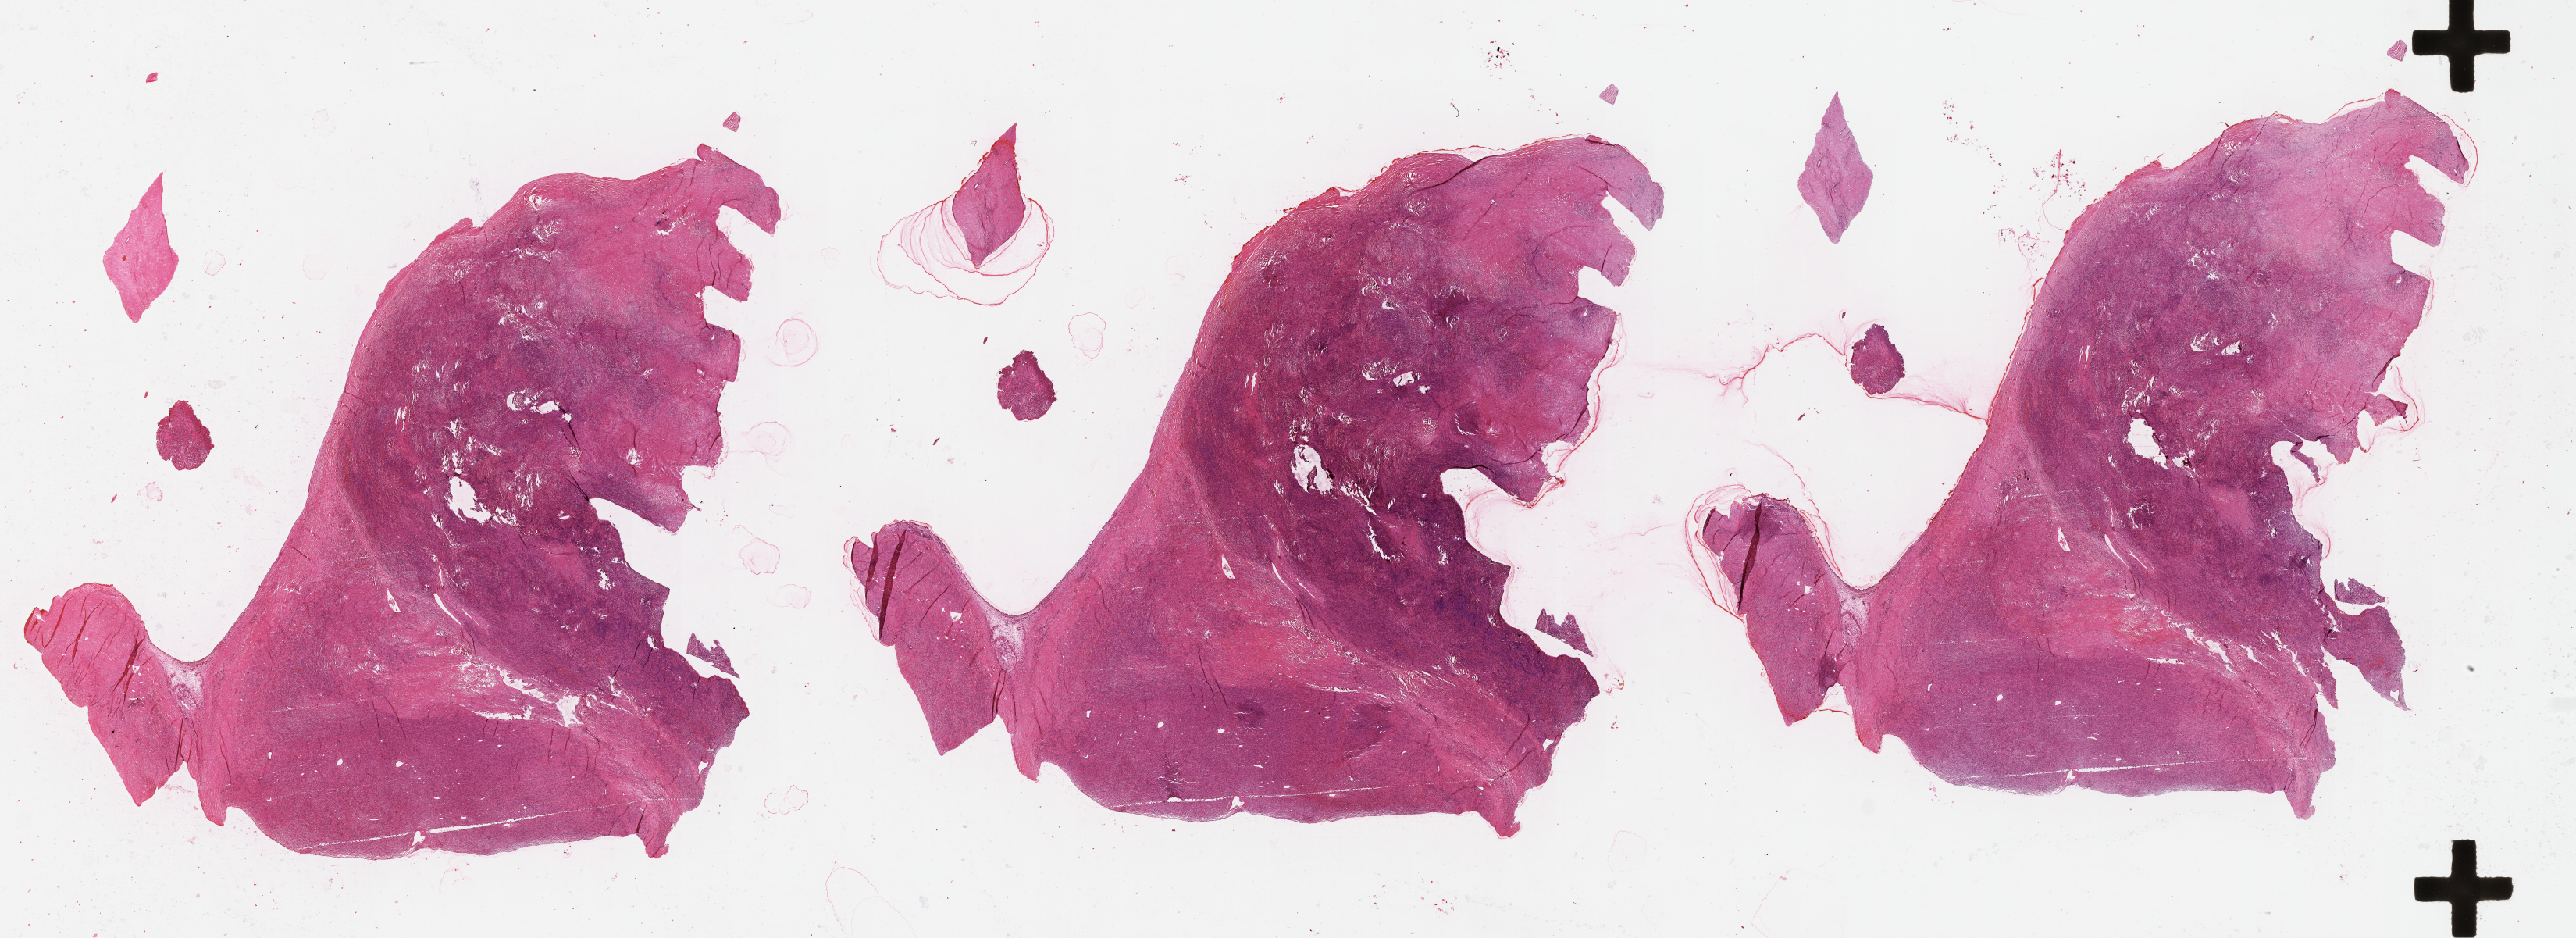
Whole-slide histology image, H&E-stained — whole scanned area (about 53.1 x 19.3 mm) shown as a low-resolution overview; tumour tissue sample. Male, 62 y/o.
Primary tumour site (as recorded): chest. Patient diagnosis (cohort enrolment): sarcoma (site not recorded at cohort level).